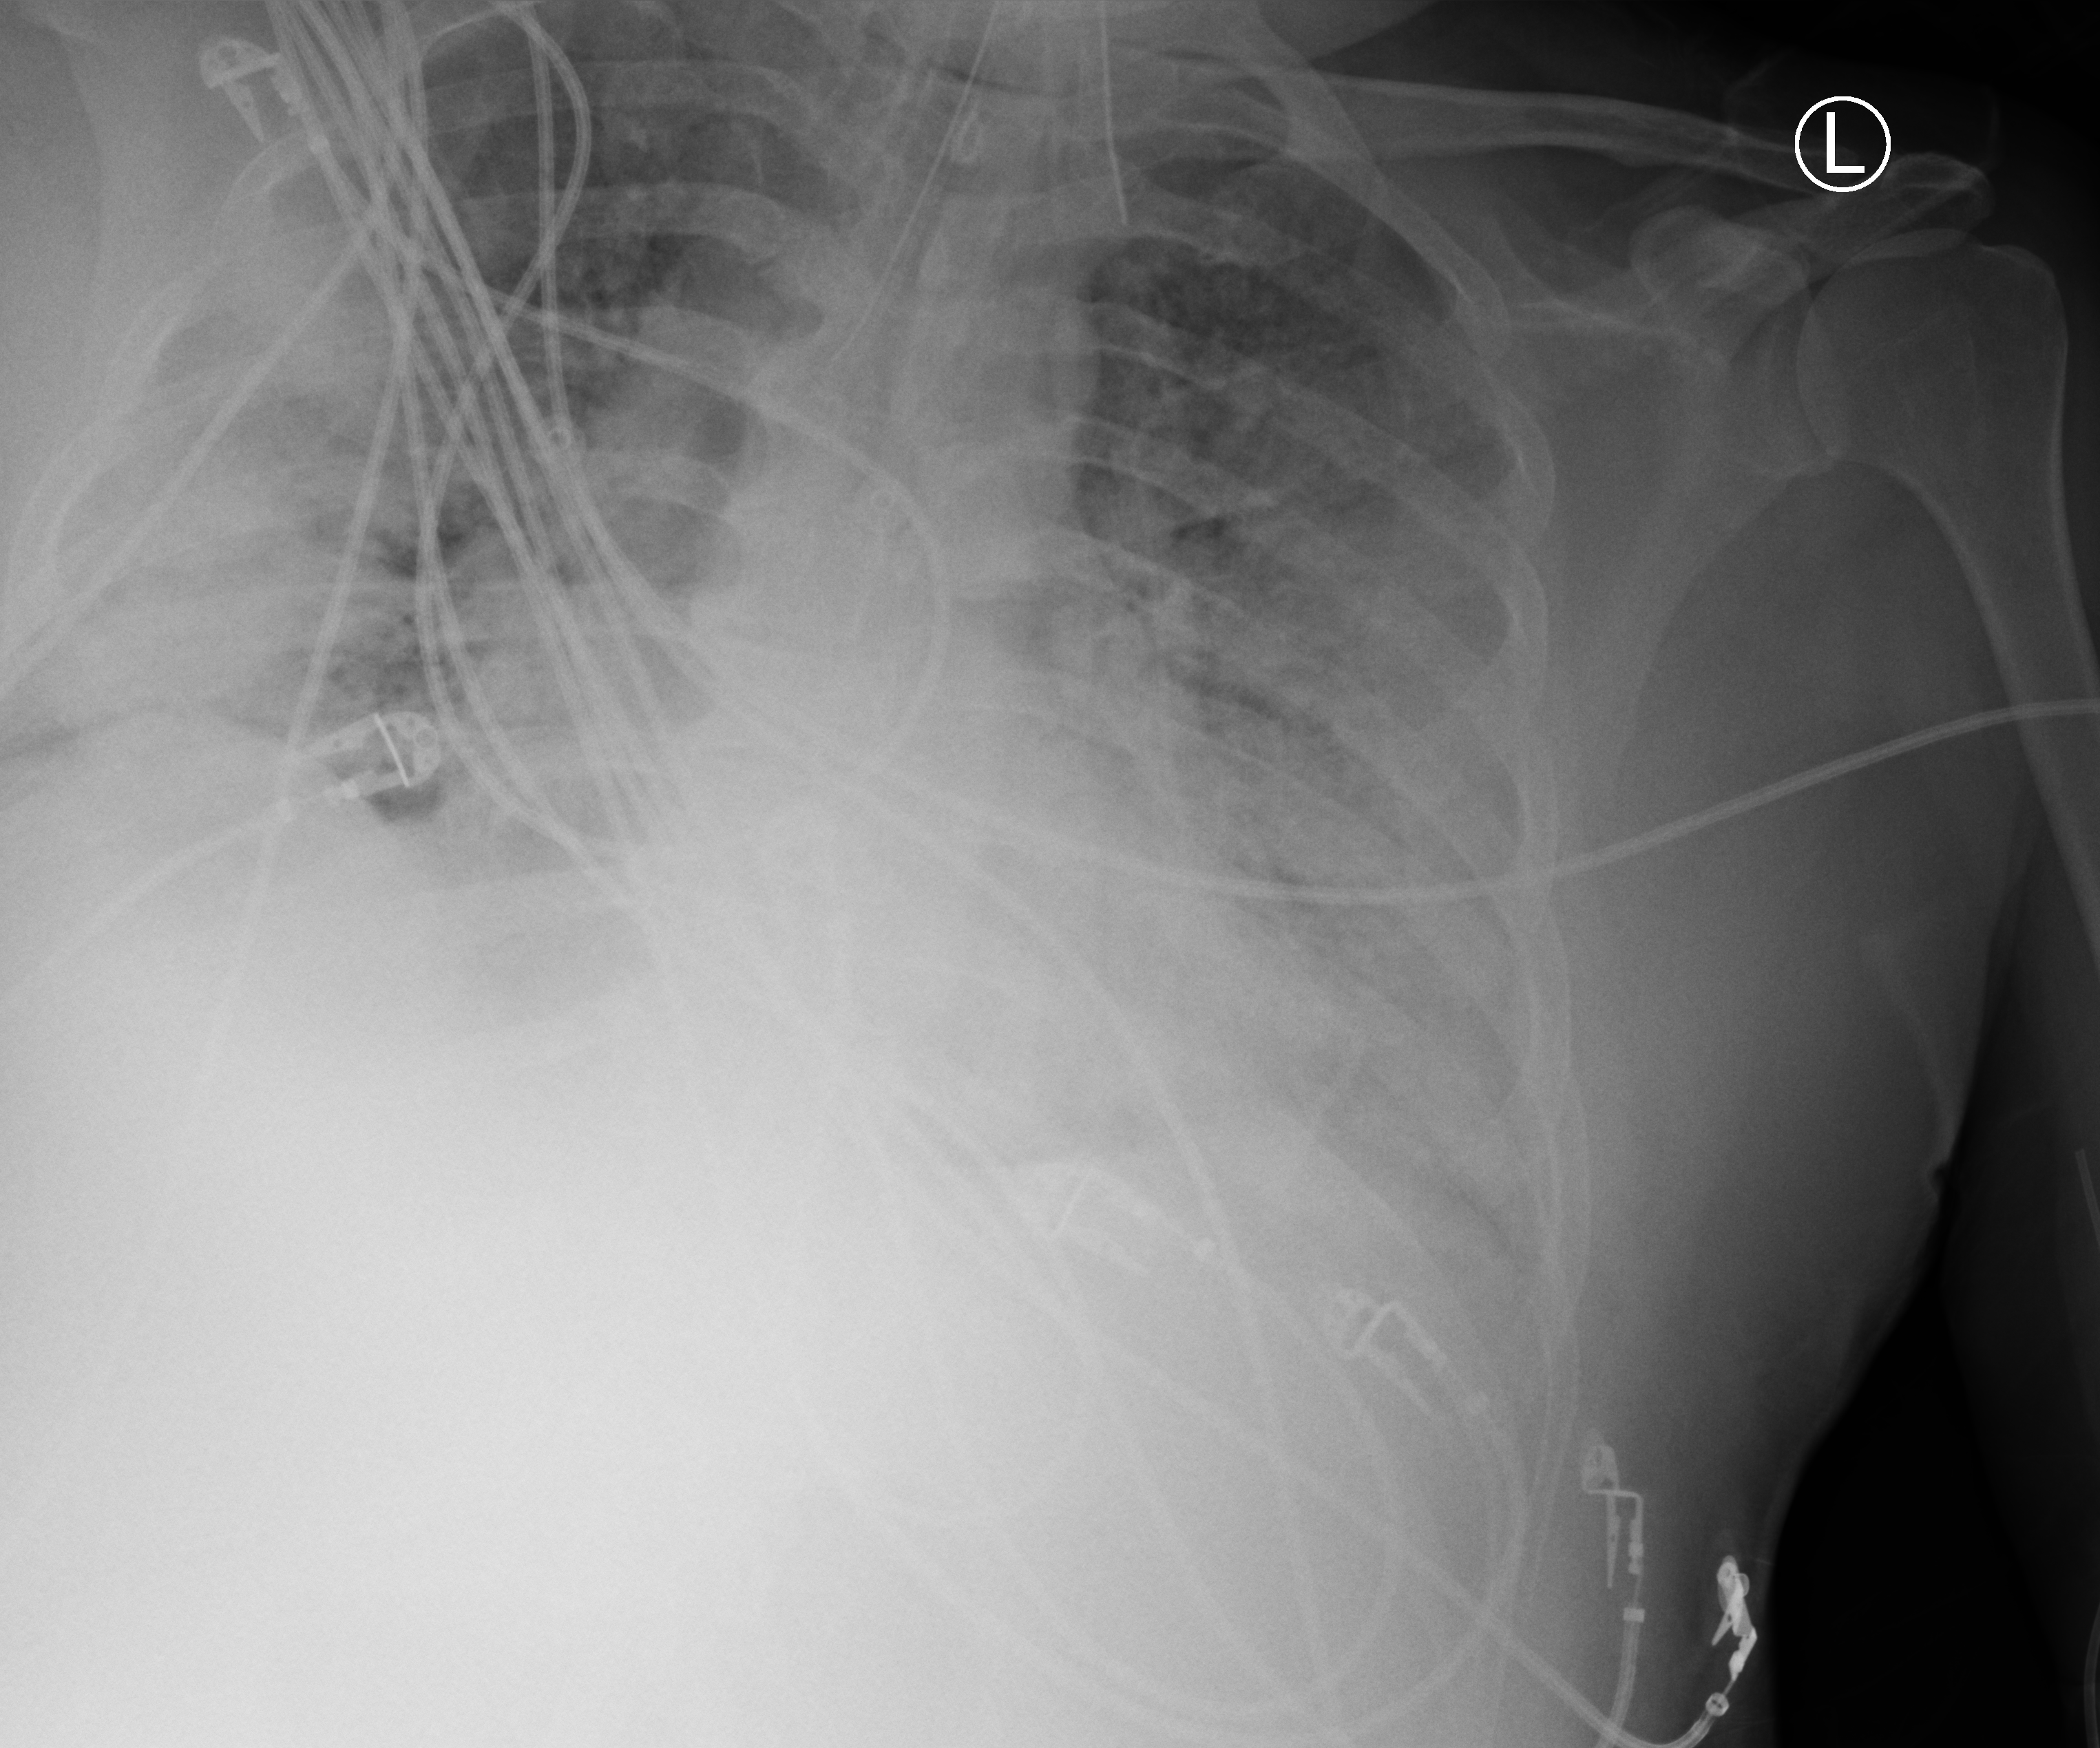
Portable chest radiograph; anteroposterior (AP) projection. Male patient hospitalised with COVID-19, age 18–59 years.
From the hospital-stay record, not from the radiograph (when in the stay this image was taken is not recorded):
- mechanically ventilated during this hospital stay: yes